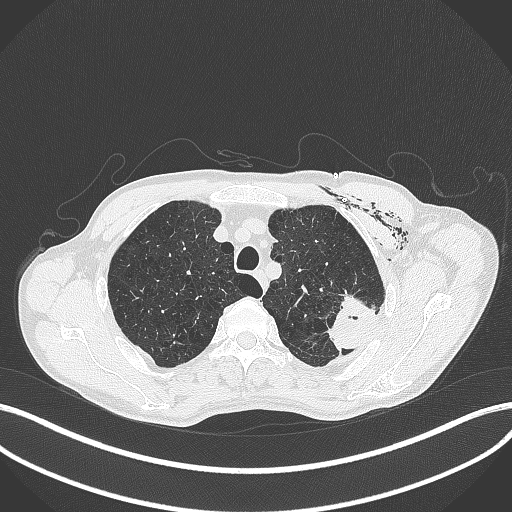
Chest CT, one axial slice. Slice 337 of 457 in the series (ordered by position). Reconstruction kernel B70f. 120 kVp. Lung window (W 1500 / L -600 HU). 1 mm slice thickness. 512 × 512 image matrix, field of view 400 × 400 mm. Male patient, age 58 years. Case-level facts recorded for this patient, not image findings: clinical TNM (as recorded): T3 N0 M0.
Structures marked on this image (bounding box drawn by a radiologist):
- lung tumour (recorded histology: adenocarcinoma): bounding box <319,289,380,347> (left, top, right, bottom; pixels)